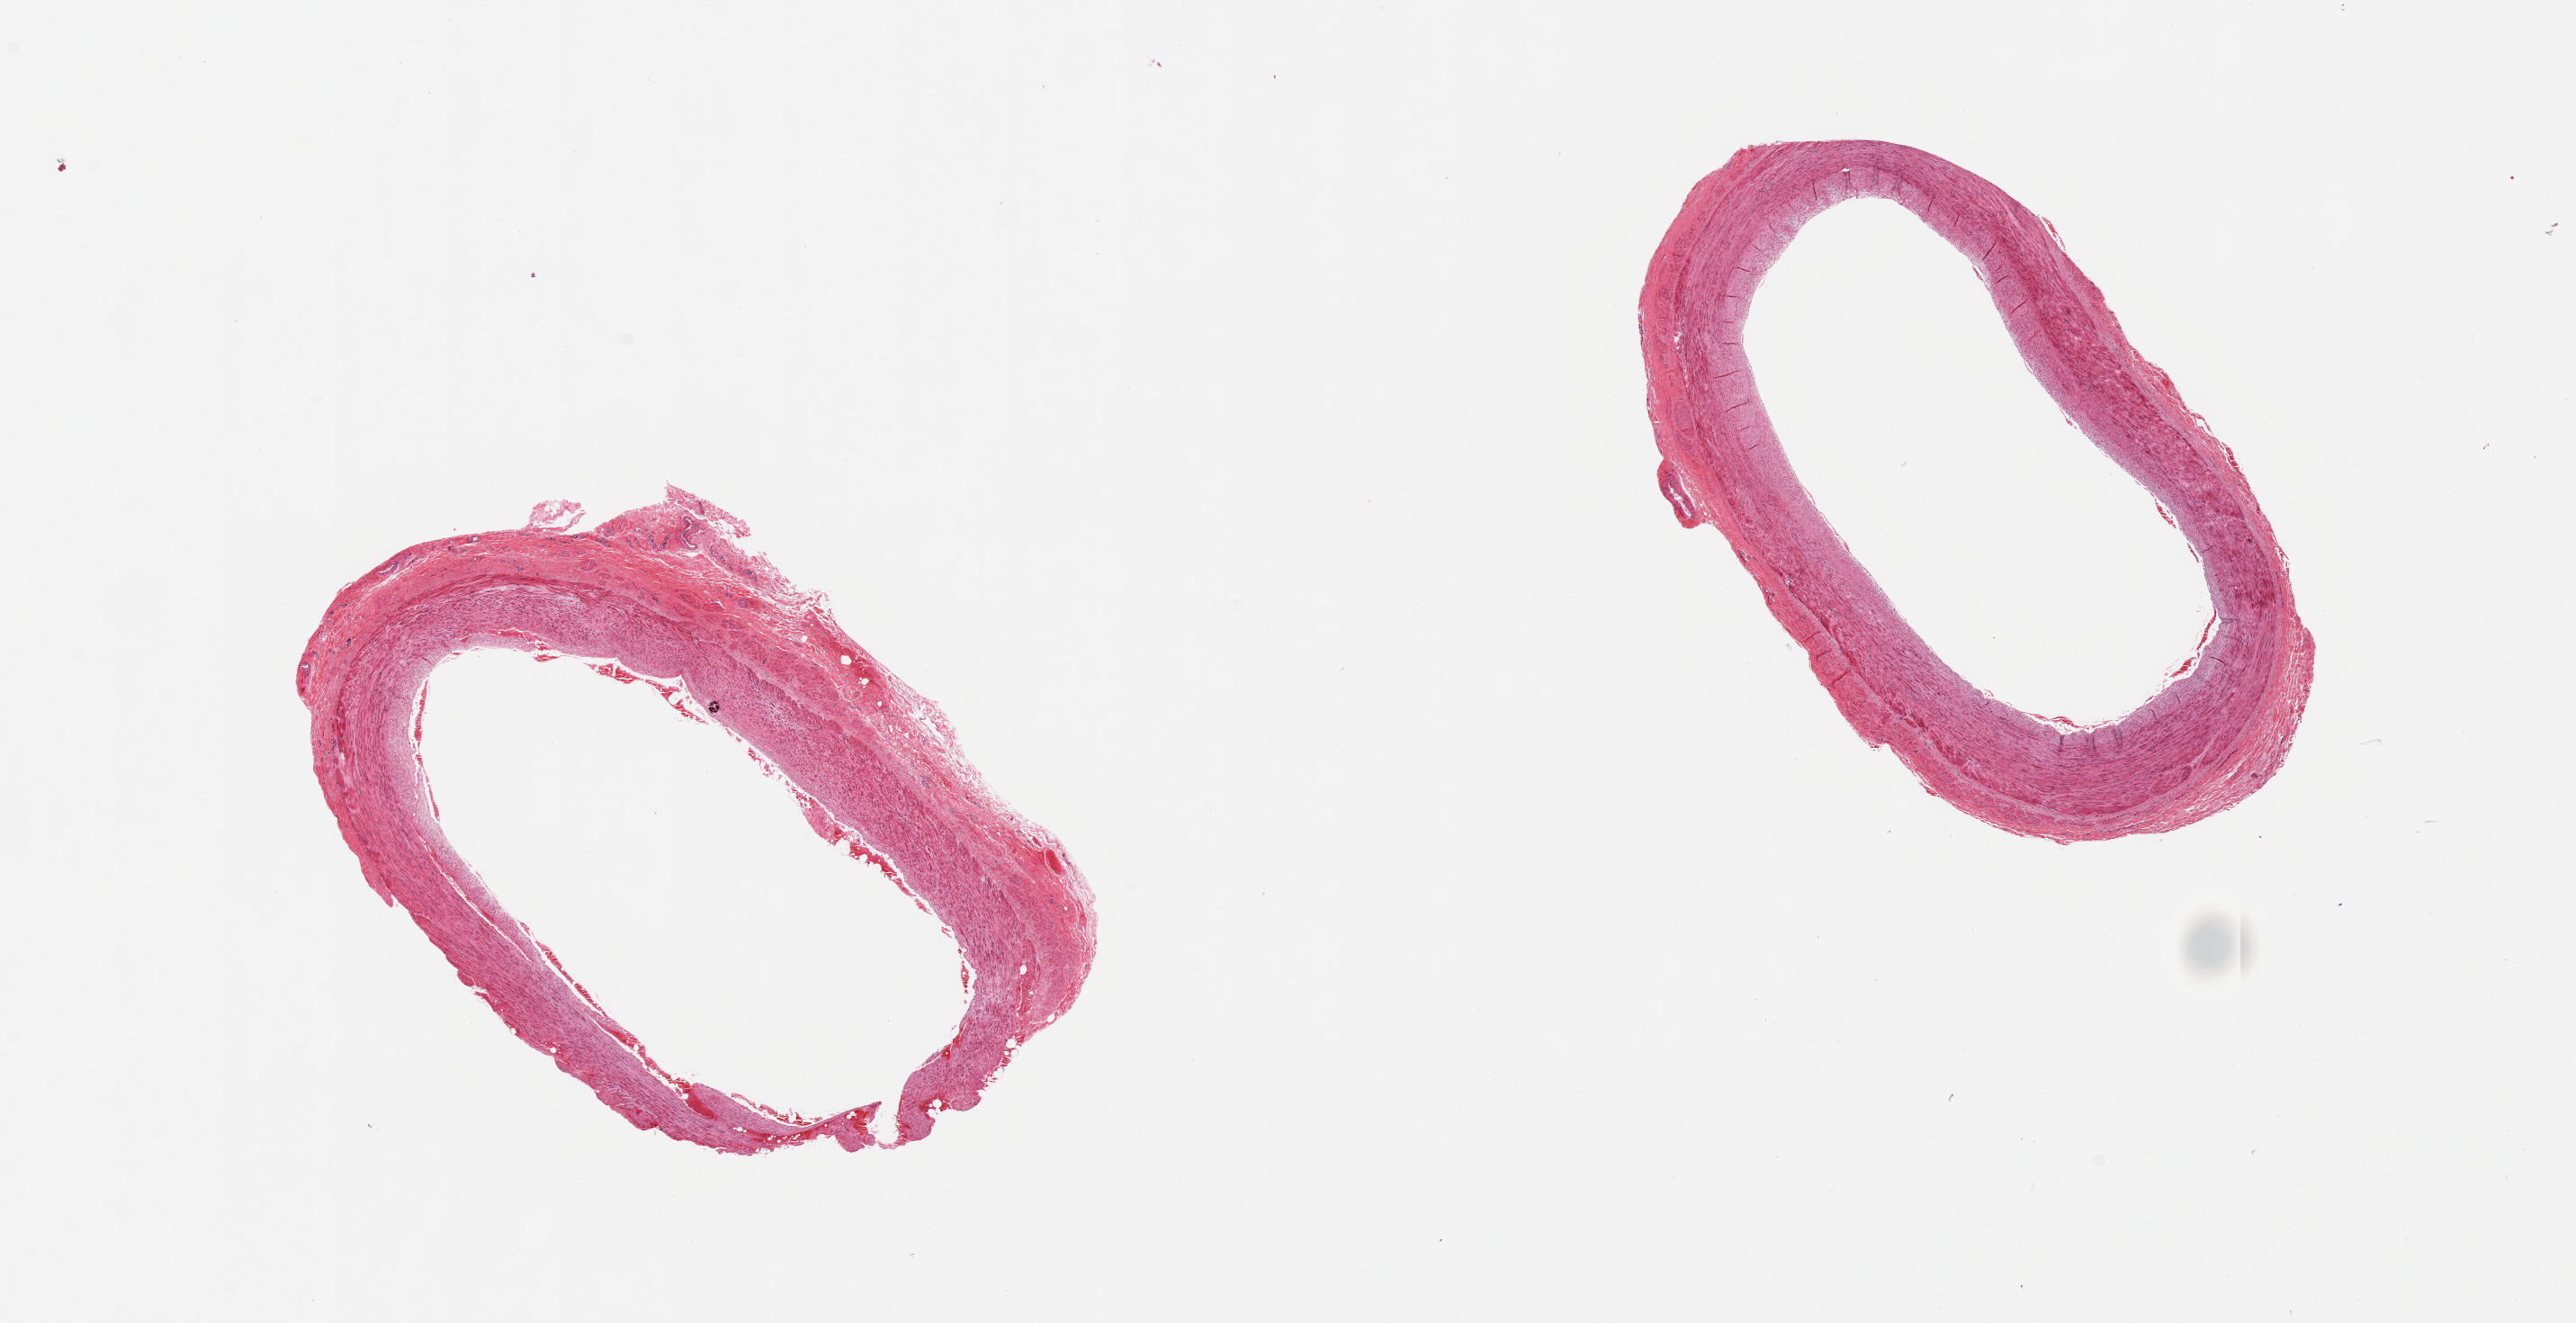
Digitized haematoxylin and eosin-stained section, whole scanned area (about 22.6 x 11.6 mm) shown as a low-resolution overview, PAXgene-fixed paraffin-embedded (PFPE) section, section of tibial artery (target tissue), donor tissue sample. Male donor.
Pathologist's review note for this sample: 2 pieces, clean specimens.